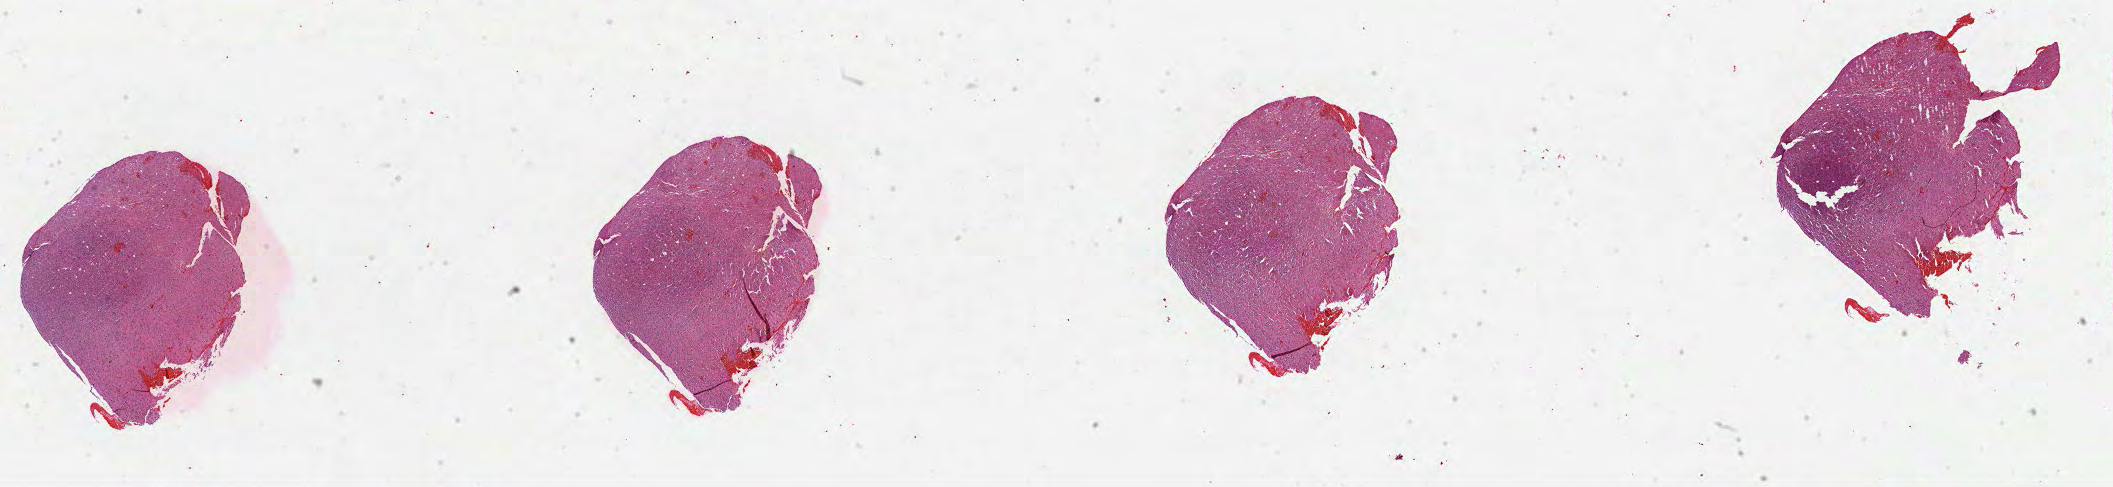
Whole-slide histology image, H&E, shown as a low-resolution overview of the whole scanned area (about 34.1 x 7.9 mm, slide scanned at 40x), formalin-fixed paraffin-embedded (FFPE) diagnostic section, brain, primary tumour sample. Female patient; age at initial diagnosis 47 years. Histologic grade: G2 (moderately differentiated).
• laterality: right
• diagnosis: Oligodendroglioma, NOS